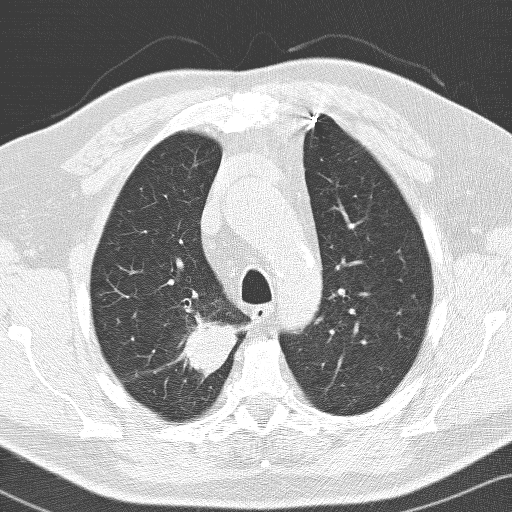
Low-dose screening chest CT, one axial slice; lung window (W 1500 / L -600 HU); 512 × 512 image matrix.
Annotated regions visible in this slice (expert manual segmentation):
- lesion 1 (tumor, upper lobe of right lung): bounding box [x1, y1, x2, y2] px = [177, 313, 238, 377]